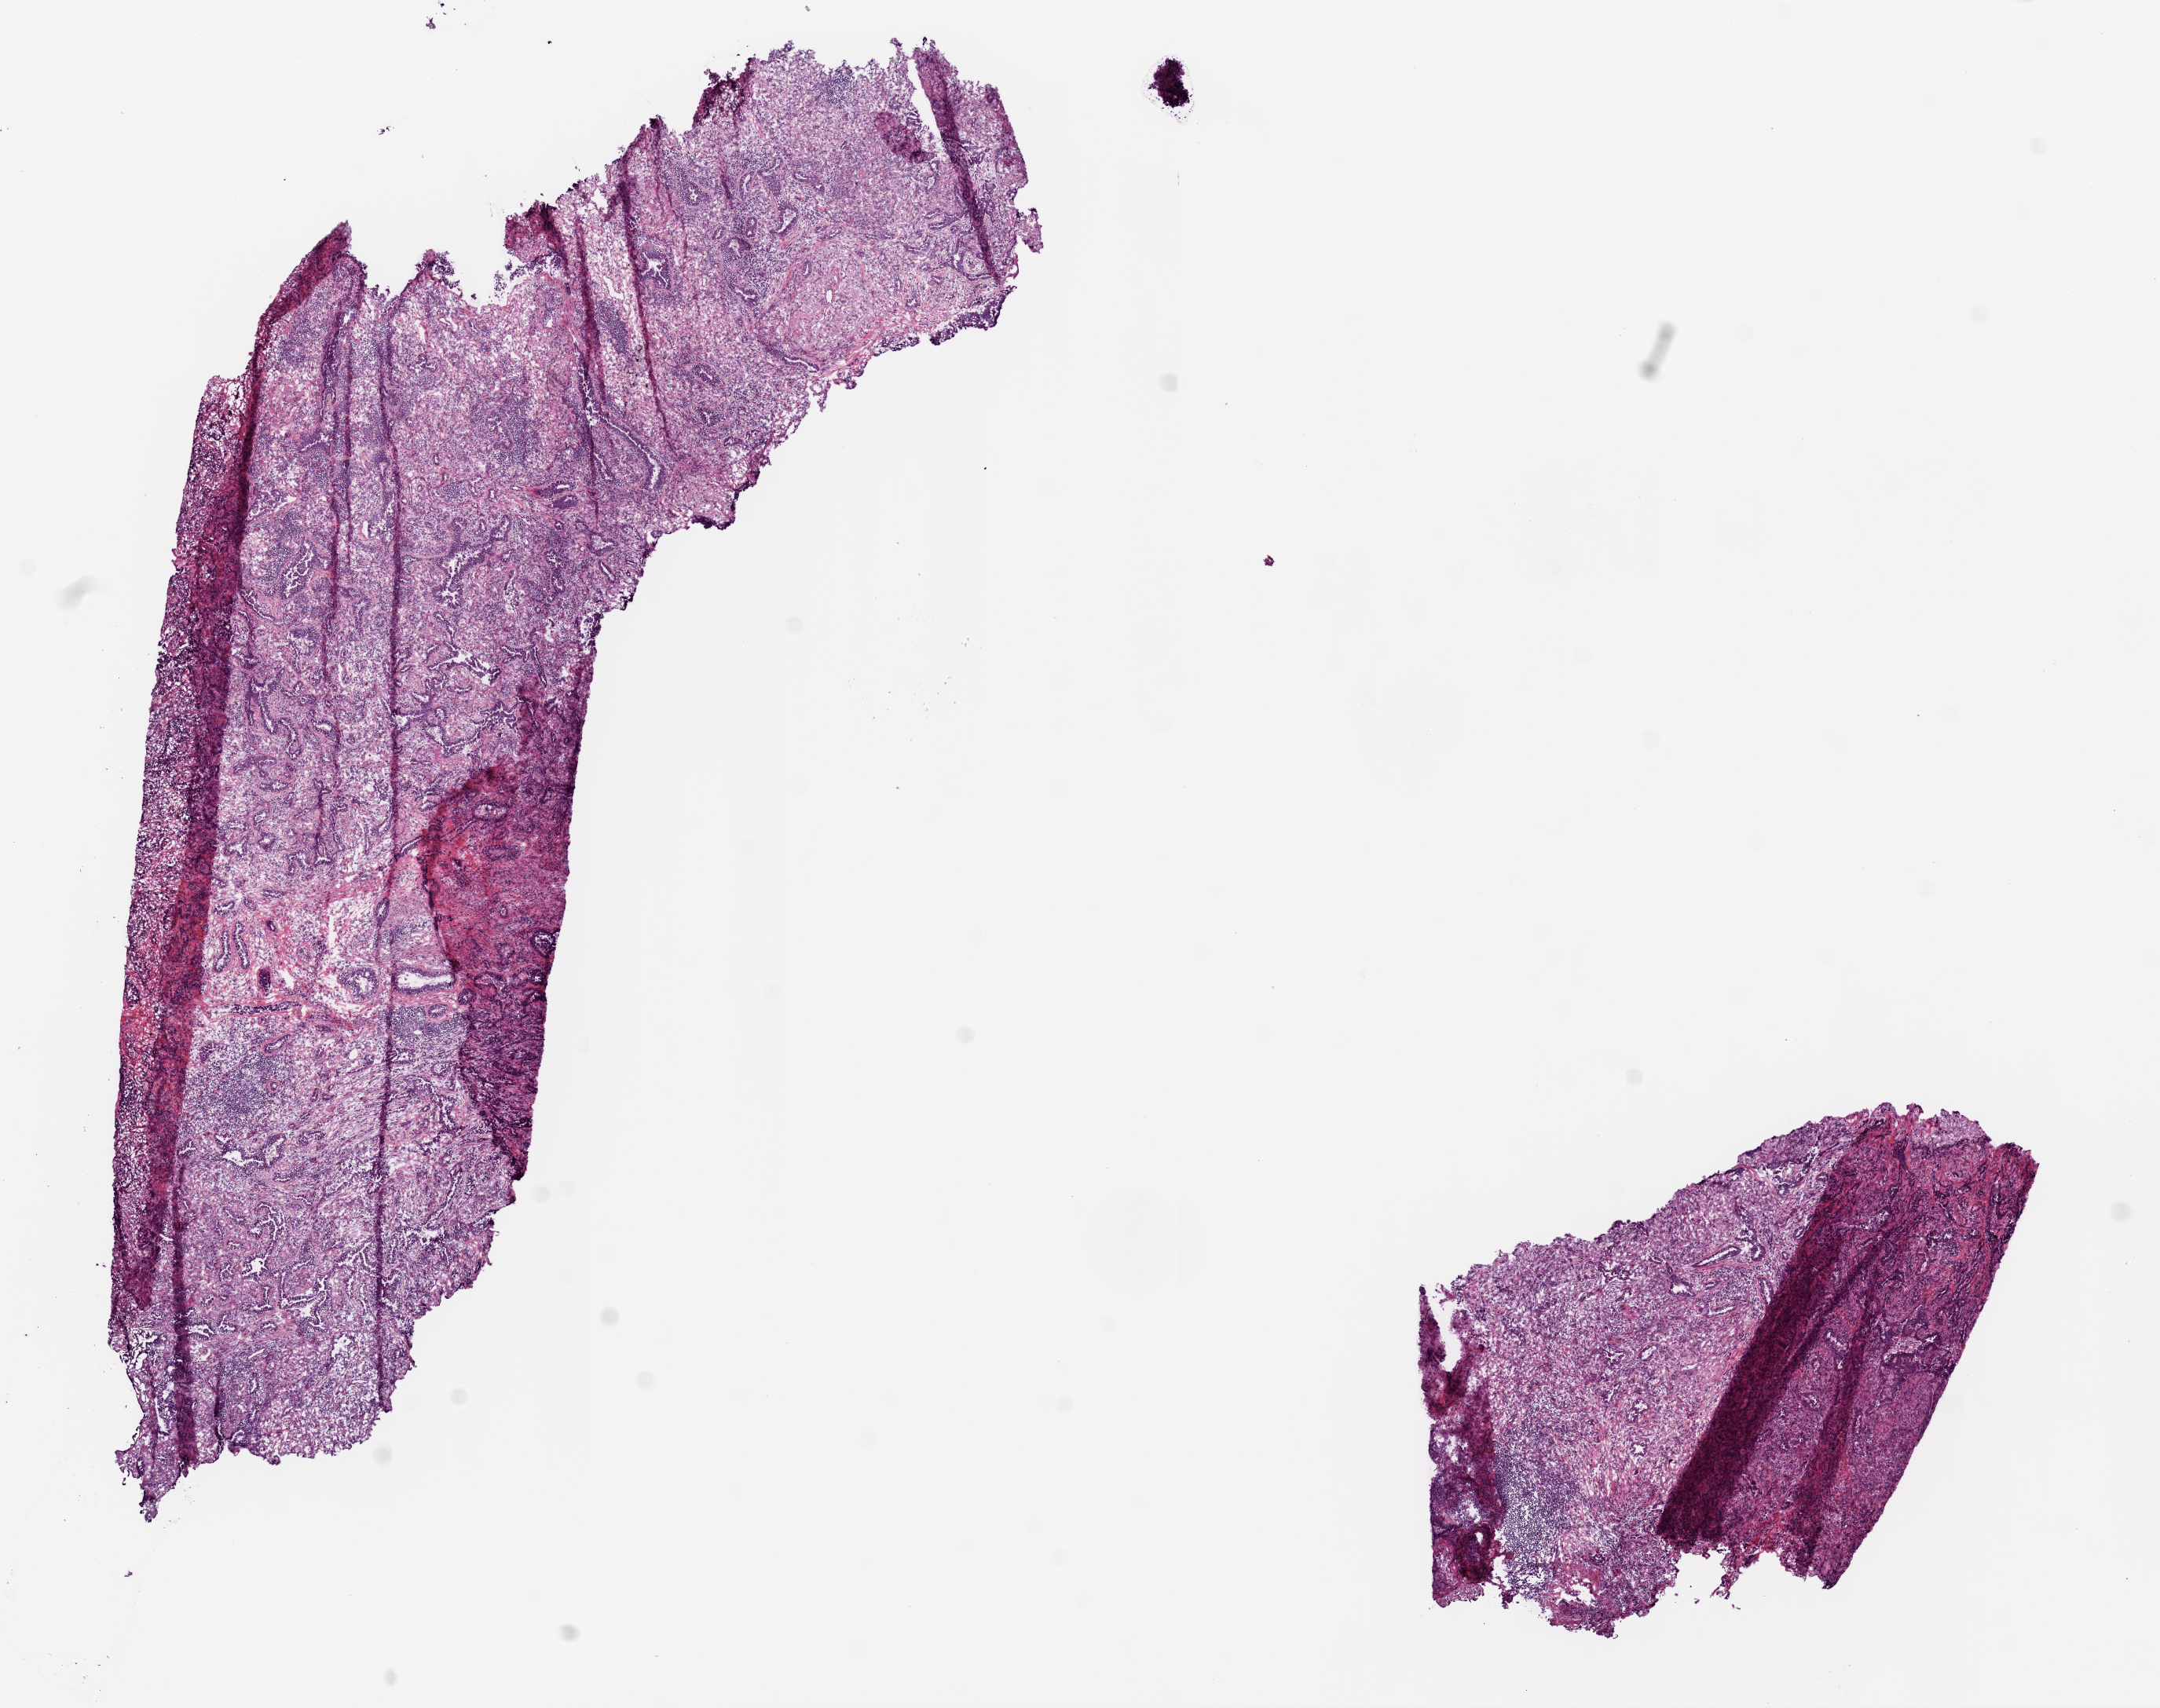
H&E-stained whole-slide image — low-resolution overview of the scanned area, about 11.0 x 8.7 mm (slide scanned at 20x), frozen section from the top of the tissue portion, lung, primary tumour sample. Female, age 82 years at initial diagnosis. Pathologist review of this section (percent, as recorded): tumour cells 78%, tumour nuclei 70%, normal cells 0%, stromal cells 20%, necrosis 2%.
- AJCC pathologic stage: IB
- diagnosis: Adenocarcinoma, NOS (upper lobe, lung)